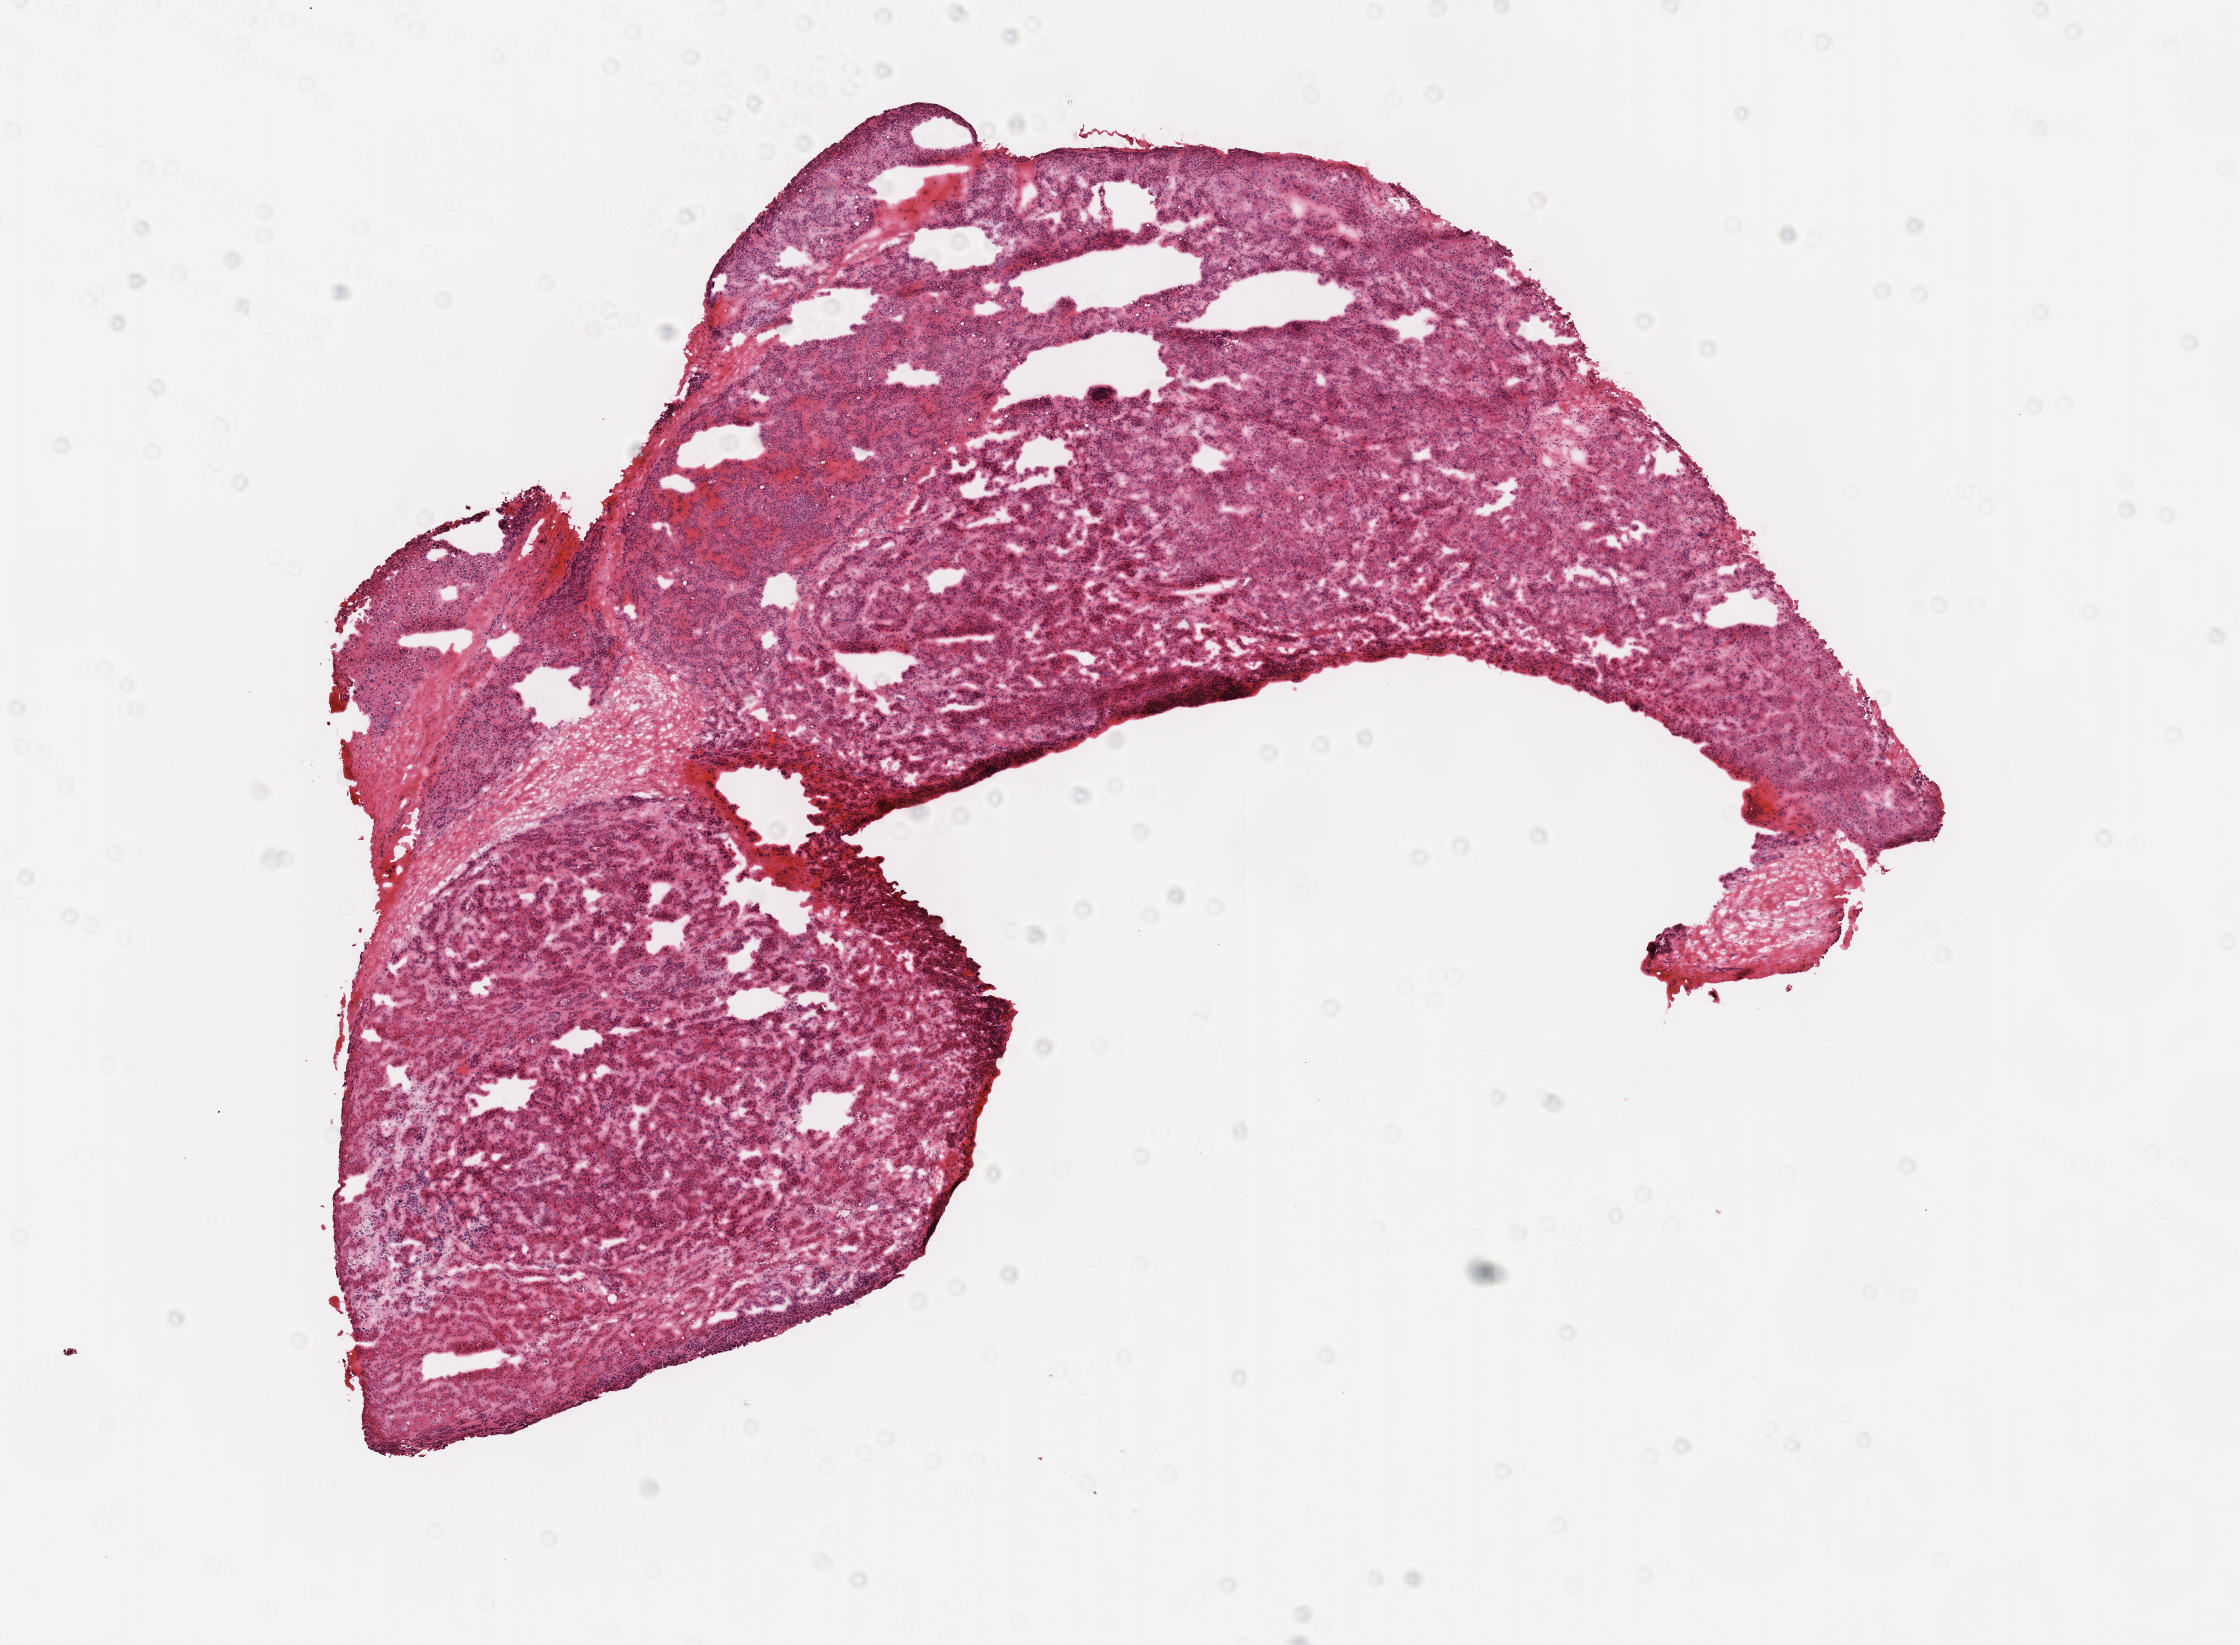
Whole-slide histology image, H&E — whole scanned area (about 9.1 x 6.7 mm, from a 40x scan) shown as a low-resolution overview, frozen section from the top of the tissue portion, liver, primary tumour sample. Male, age 50 years at initial diagnosis. Histologic grade: G3 (poorly differentiated). Composition of this section per pathologist review: tumour cells 100%, tumour nuclei 75%, normal cells 0%, stromal cells 0%, necrosis 0%. Infiltration values recorded for this section: lymphocyte infiltration 2%, monocyte infiltration 0%, neutrophil infiltration 0%.
TNM: T1 N0 M0. Histologic diagnosis: Hepatocellular carcinoma, NOS. AJCC pathologic stage: I (7th edition).